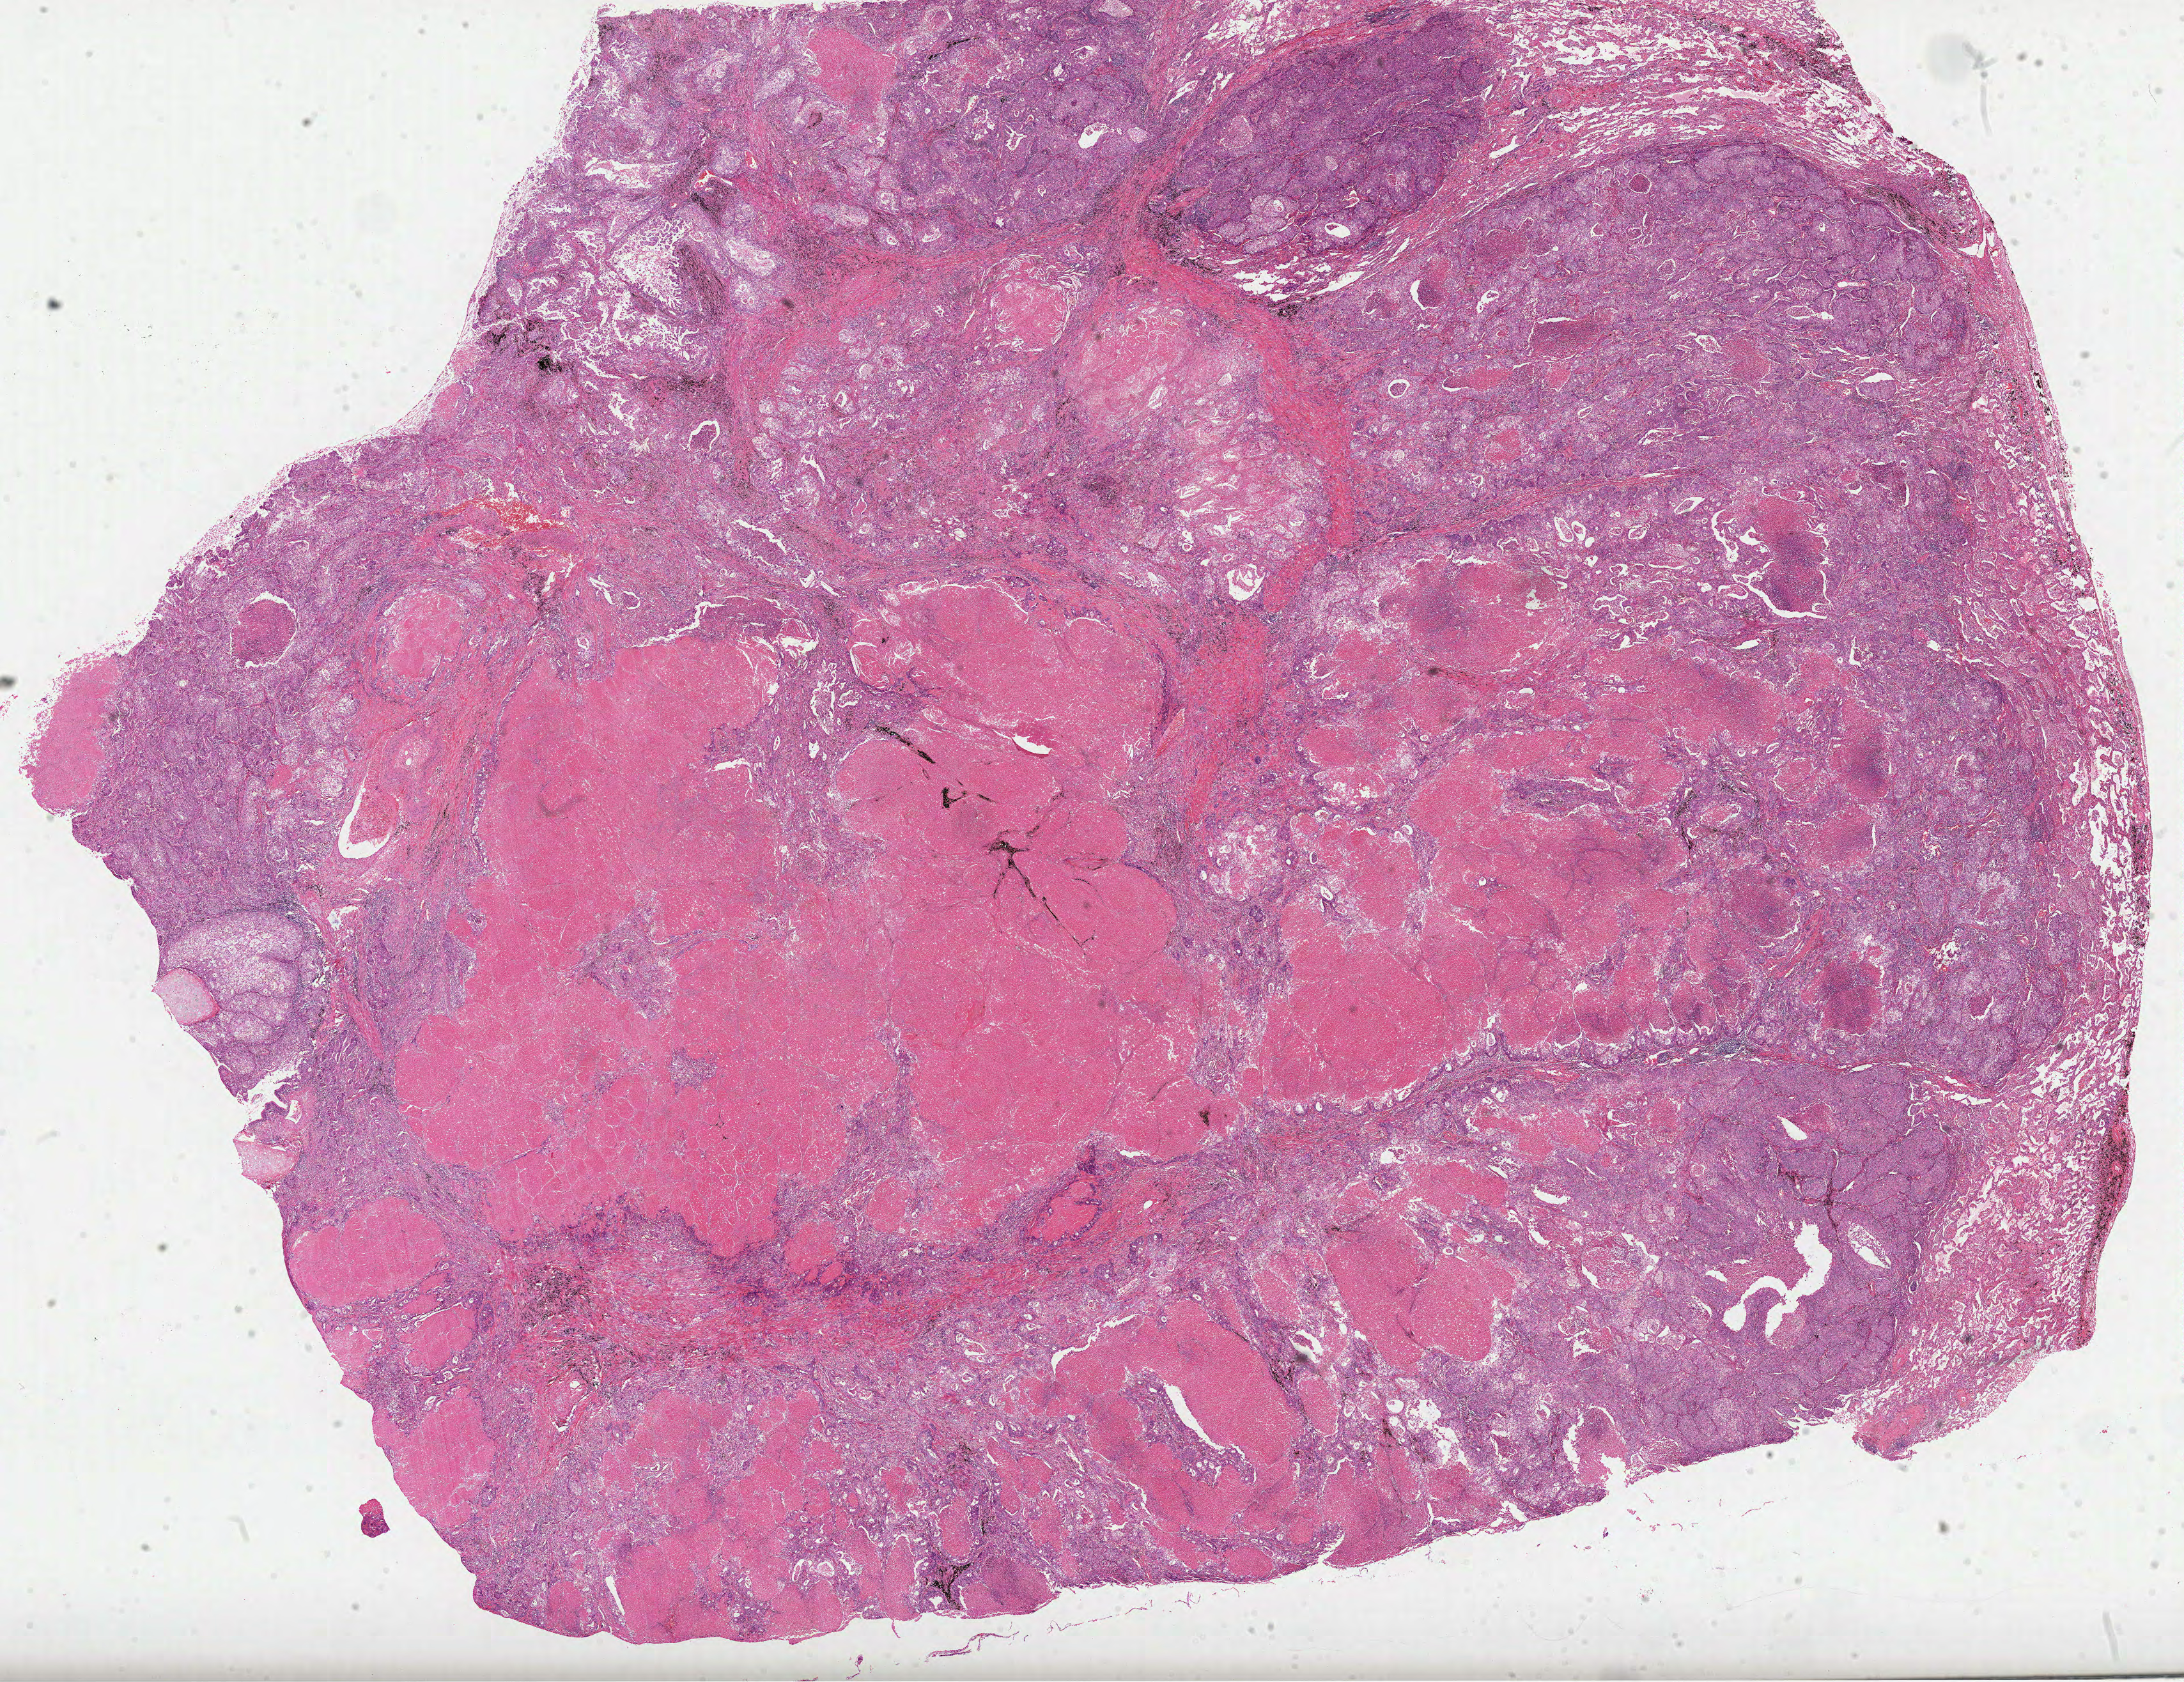
Digitized H&E-stained tissue section (whole slide) — shown as a low-resolution overview of the whole scanned area (about 27.6 x 21.2 mm, from a 40x scan); formalin-fixed paraffin-embedded (FFPE) diagnostic section; lung, primary tumour sample. Male, age 59 years at initial diagnosis.
Pathologic diagnosis: Adenocarcinoma, NOS (lower lobe, lung). AJCC pathologic stage: IIB (6th edition). TNM: T2 N1 M0.